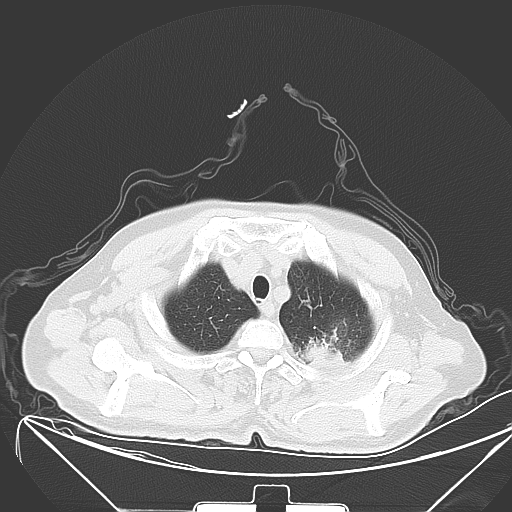
Chest CT, one axial slice; position 52 of 64 along the scan axis; lung window (W 1500 / L -600 HU); 512 × 512 image matrix, field of view 431 × 431 mm. Patient: male, 58 years. From the clinical record (not read from this slice): clinical TNM (as recorded): T2b N3 M1b.
Annotated regions visible in this slice (rectangle marked by the reading radiologist):
- lung tumour (recorded histology: adenocarcinoma): bounding box [x1, y1, x2, y2] px = [301, 329, 351, 372]